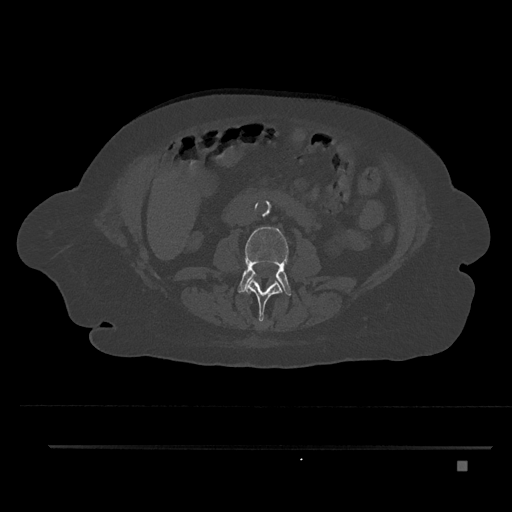
CT including the spine, one axial slice; slice 150 of 797 in the series (ordered by position); bone window (W 1800 / L 400 HU); 0.5 mm slice thickness; 512 × 512 image matrix, field of view 437 × 437 mm. Female patient, age 76 years. Case-level facts recorded for this patient, not image findings: primary cancer: lung; vertebrae with lytic lesions (as recorded): T11, L3.
Annotated regions visible in this slice (semi-automatic segmentation, software-assisted and operator-edited):
- L2 vertebra: bounding box [x1, y1, x2, y2] px = [245, 279, 282, 325]
- L3 vertebra: [238, 227, 292, 295]